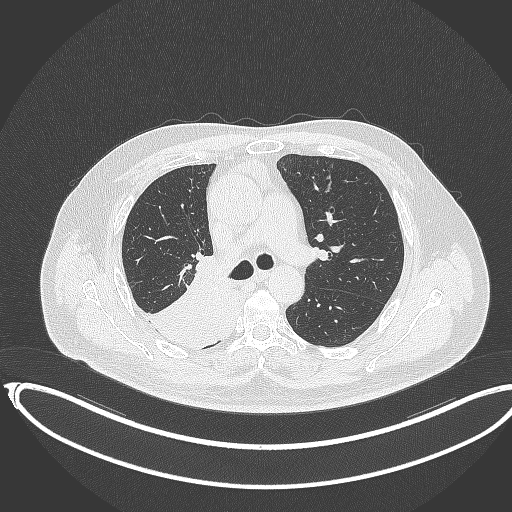
Chest CT, one axial slice; slice 232 of 403 in the series (ordered by position); reconstruction kernel B70f; lung window (W 1500 / L -600 HU); 1 mm slice thickness; 512 × 512 image matrix. Patient: male, 68 years. From the clinical record (not read from this slice): clinical TNM (as recorded): T2a N0 M0.
Annotated regions visible in this slice (rectangle marked by the reading radiologist):
- lung tumour (recorded histology: adenocarcinoma): bounding box (x1, y1, x2, y2) in pixels: (140, 253, 226, 354)